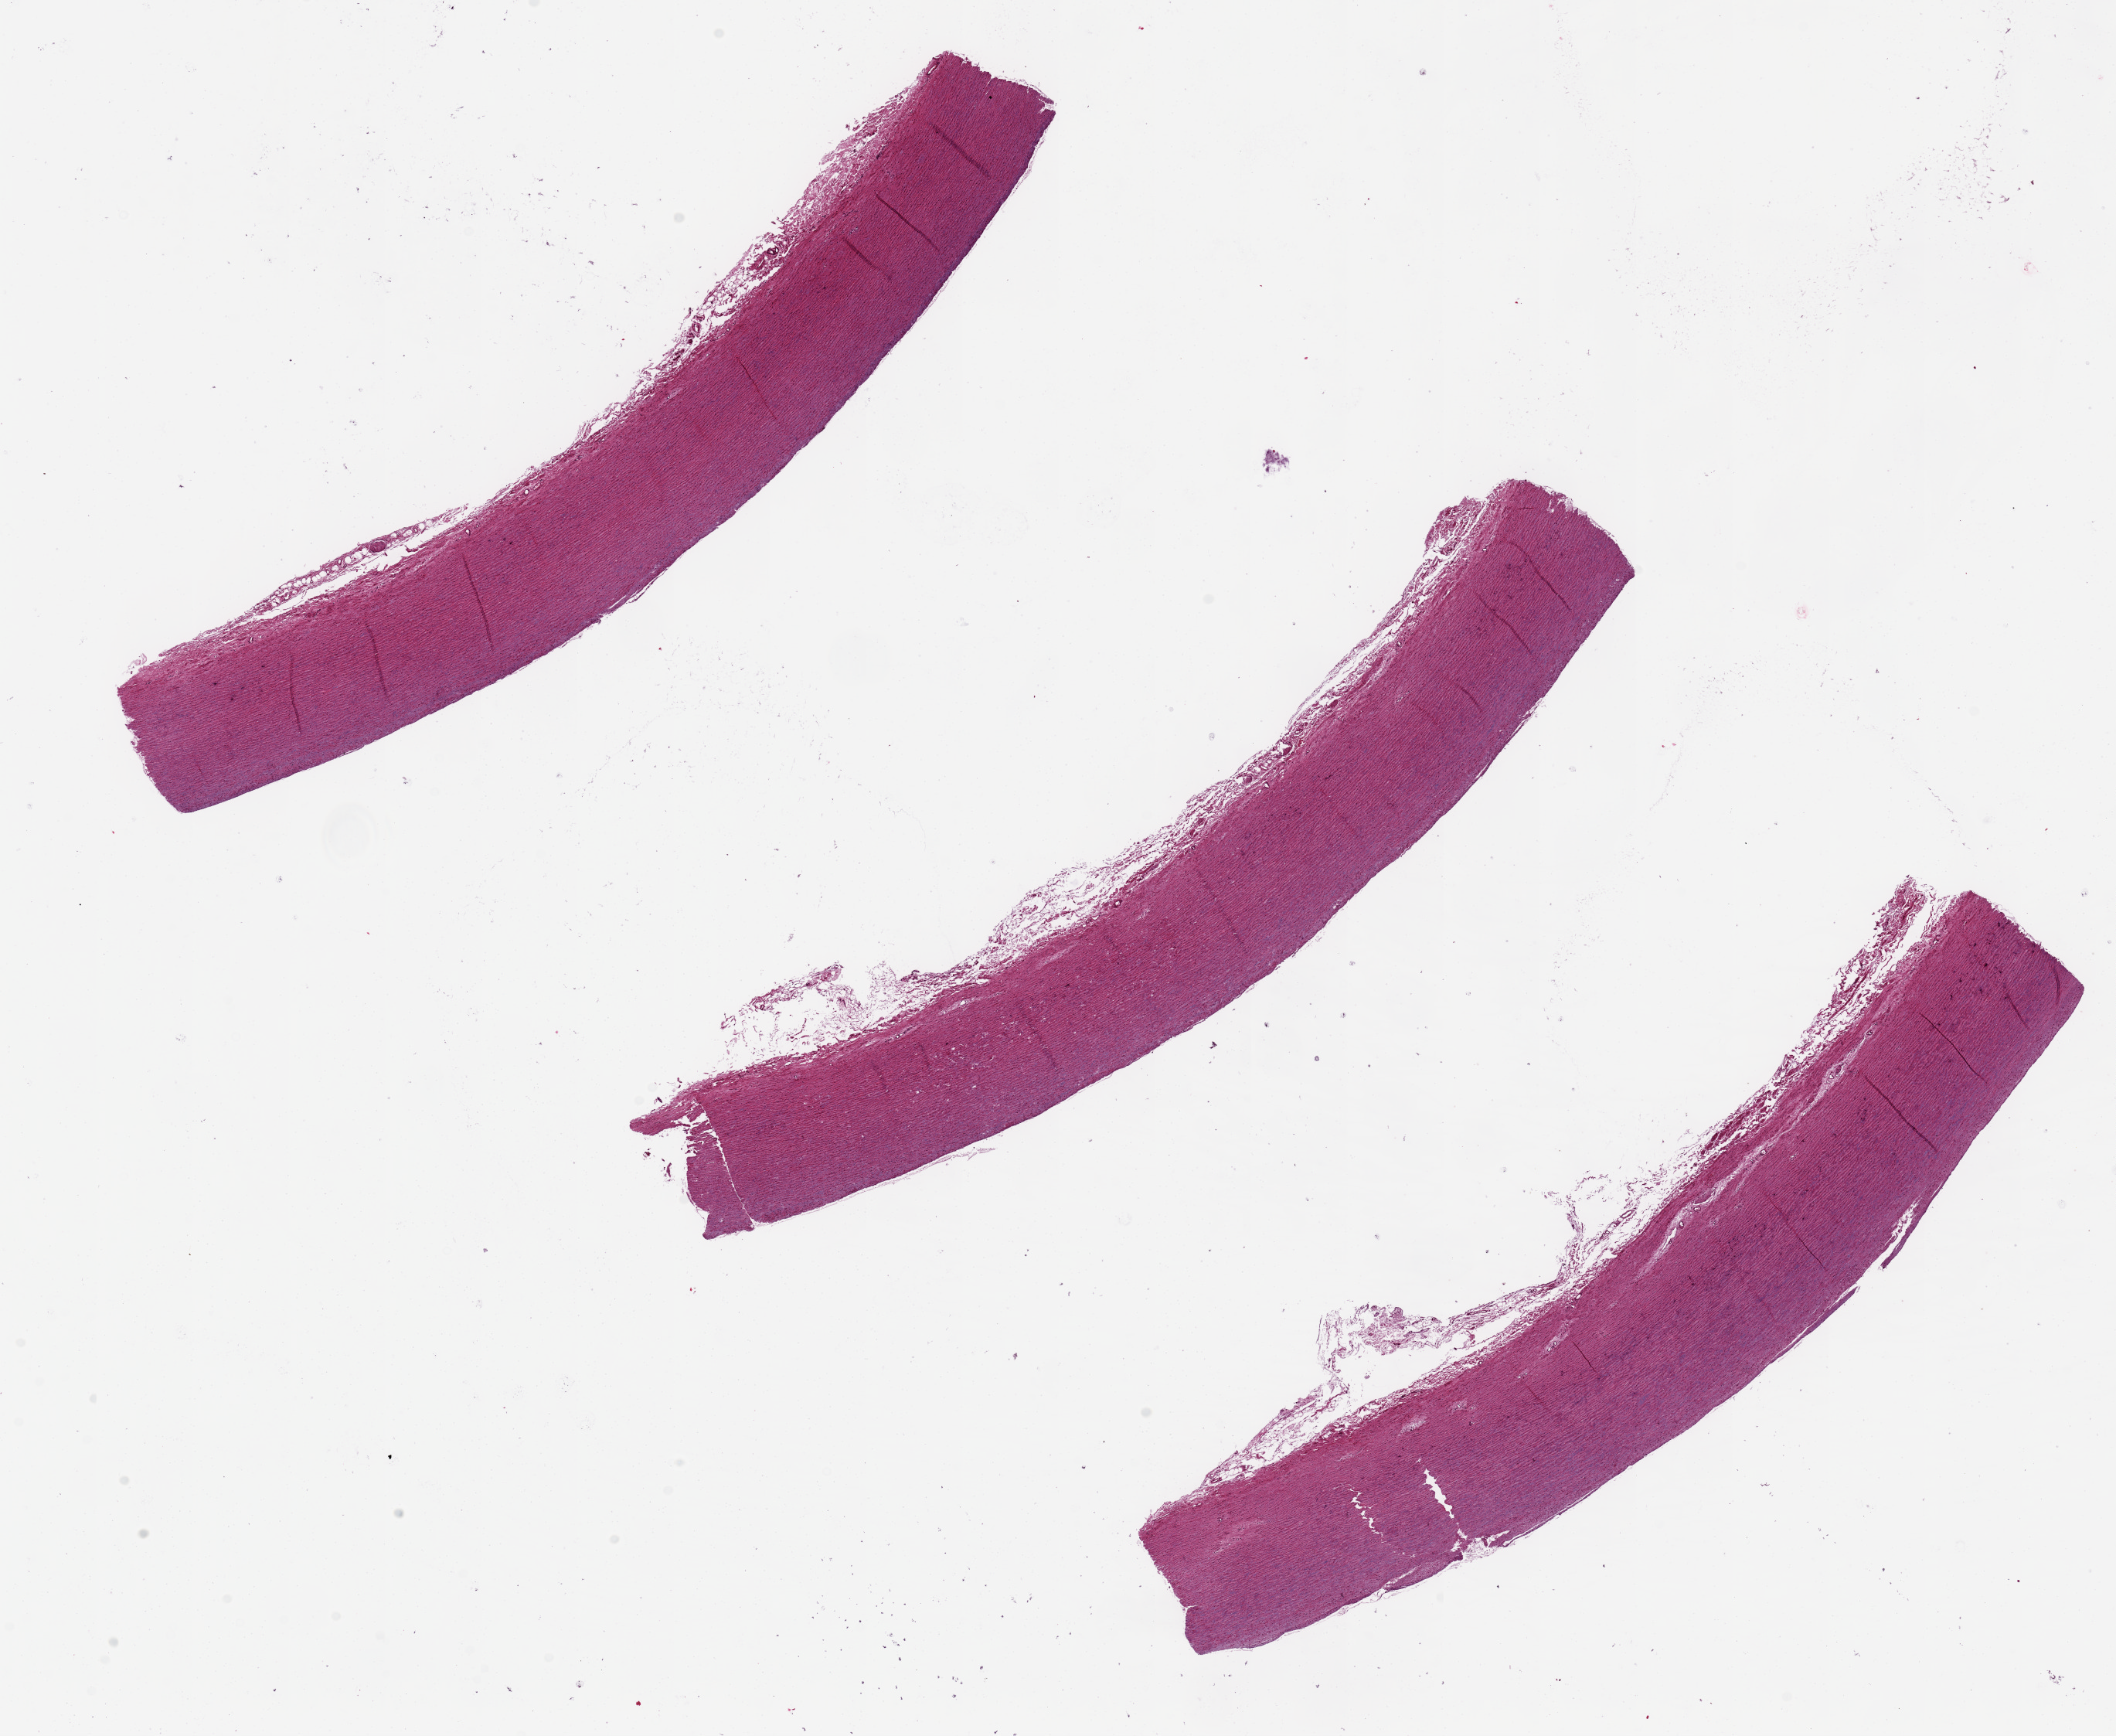
H&E whole-slide image, shown as a low-resolution overview of the whole scanned area (about 21.7 x 17.8 mm, acquisition: 20x scan). PAXgene-fixed paraffin-embedded (PFPE) section. Sampled site (target tissue): aorta. Tissue donor sample.
Review note (as recorded): 3 ~11x1.5mm pieces.